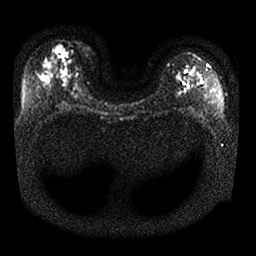
Breast MRI, one axial slice; slice 16 of 25 in the series (ordered by position); diffusion-weighted series; image 2 of 4 stored at this slice position (different b-values; order by instance number); 1.5 T; 256 × 256 image matrix, field of view 340 × 340 mm. Female patient.
Outlined on this slice (manually delineated by an expert):
- tumour on diffusion-weighted imaging: bounding box <52,44,69,58> (left, top, right, bottom; pixels)